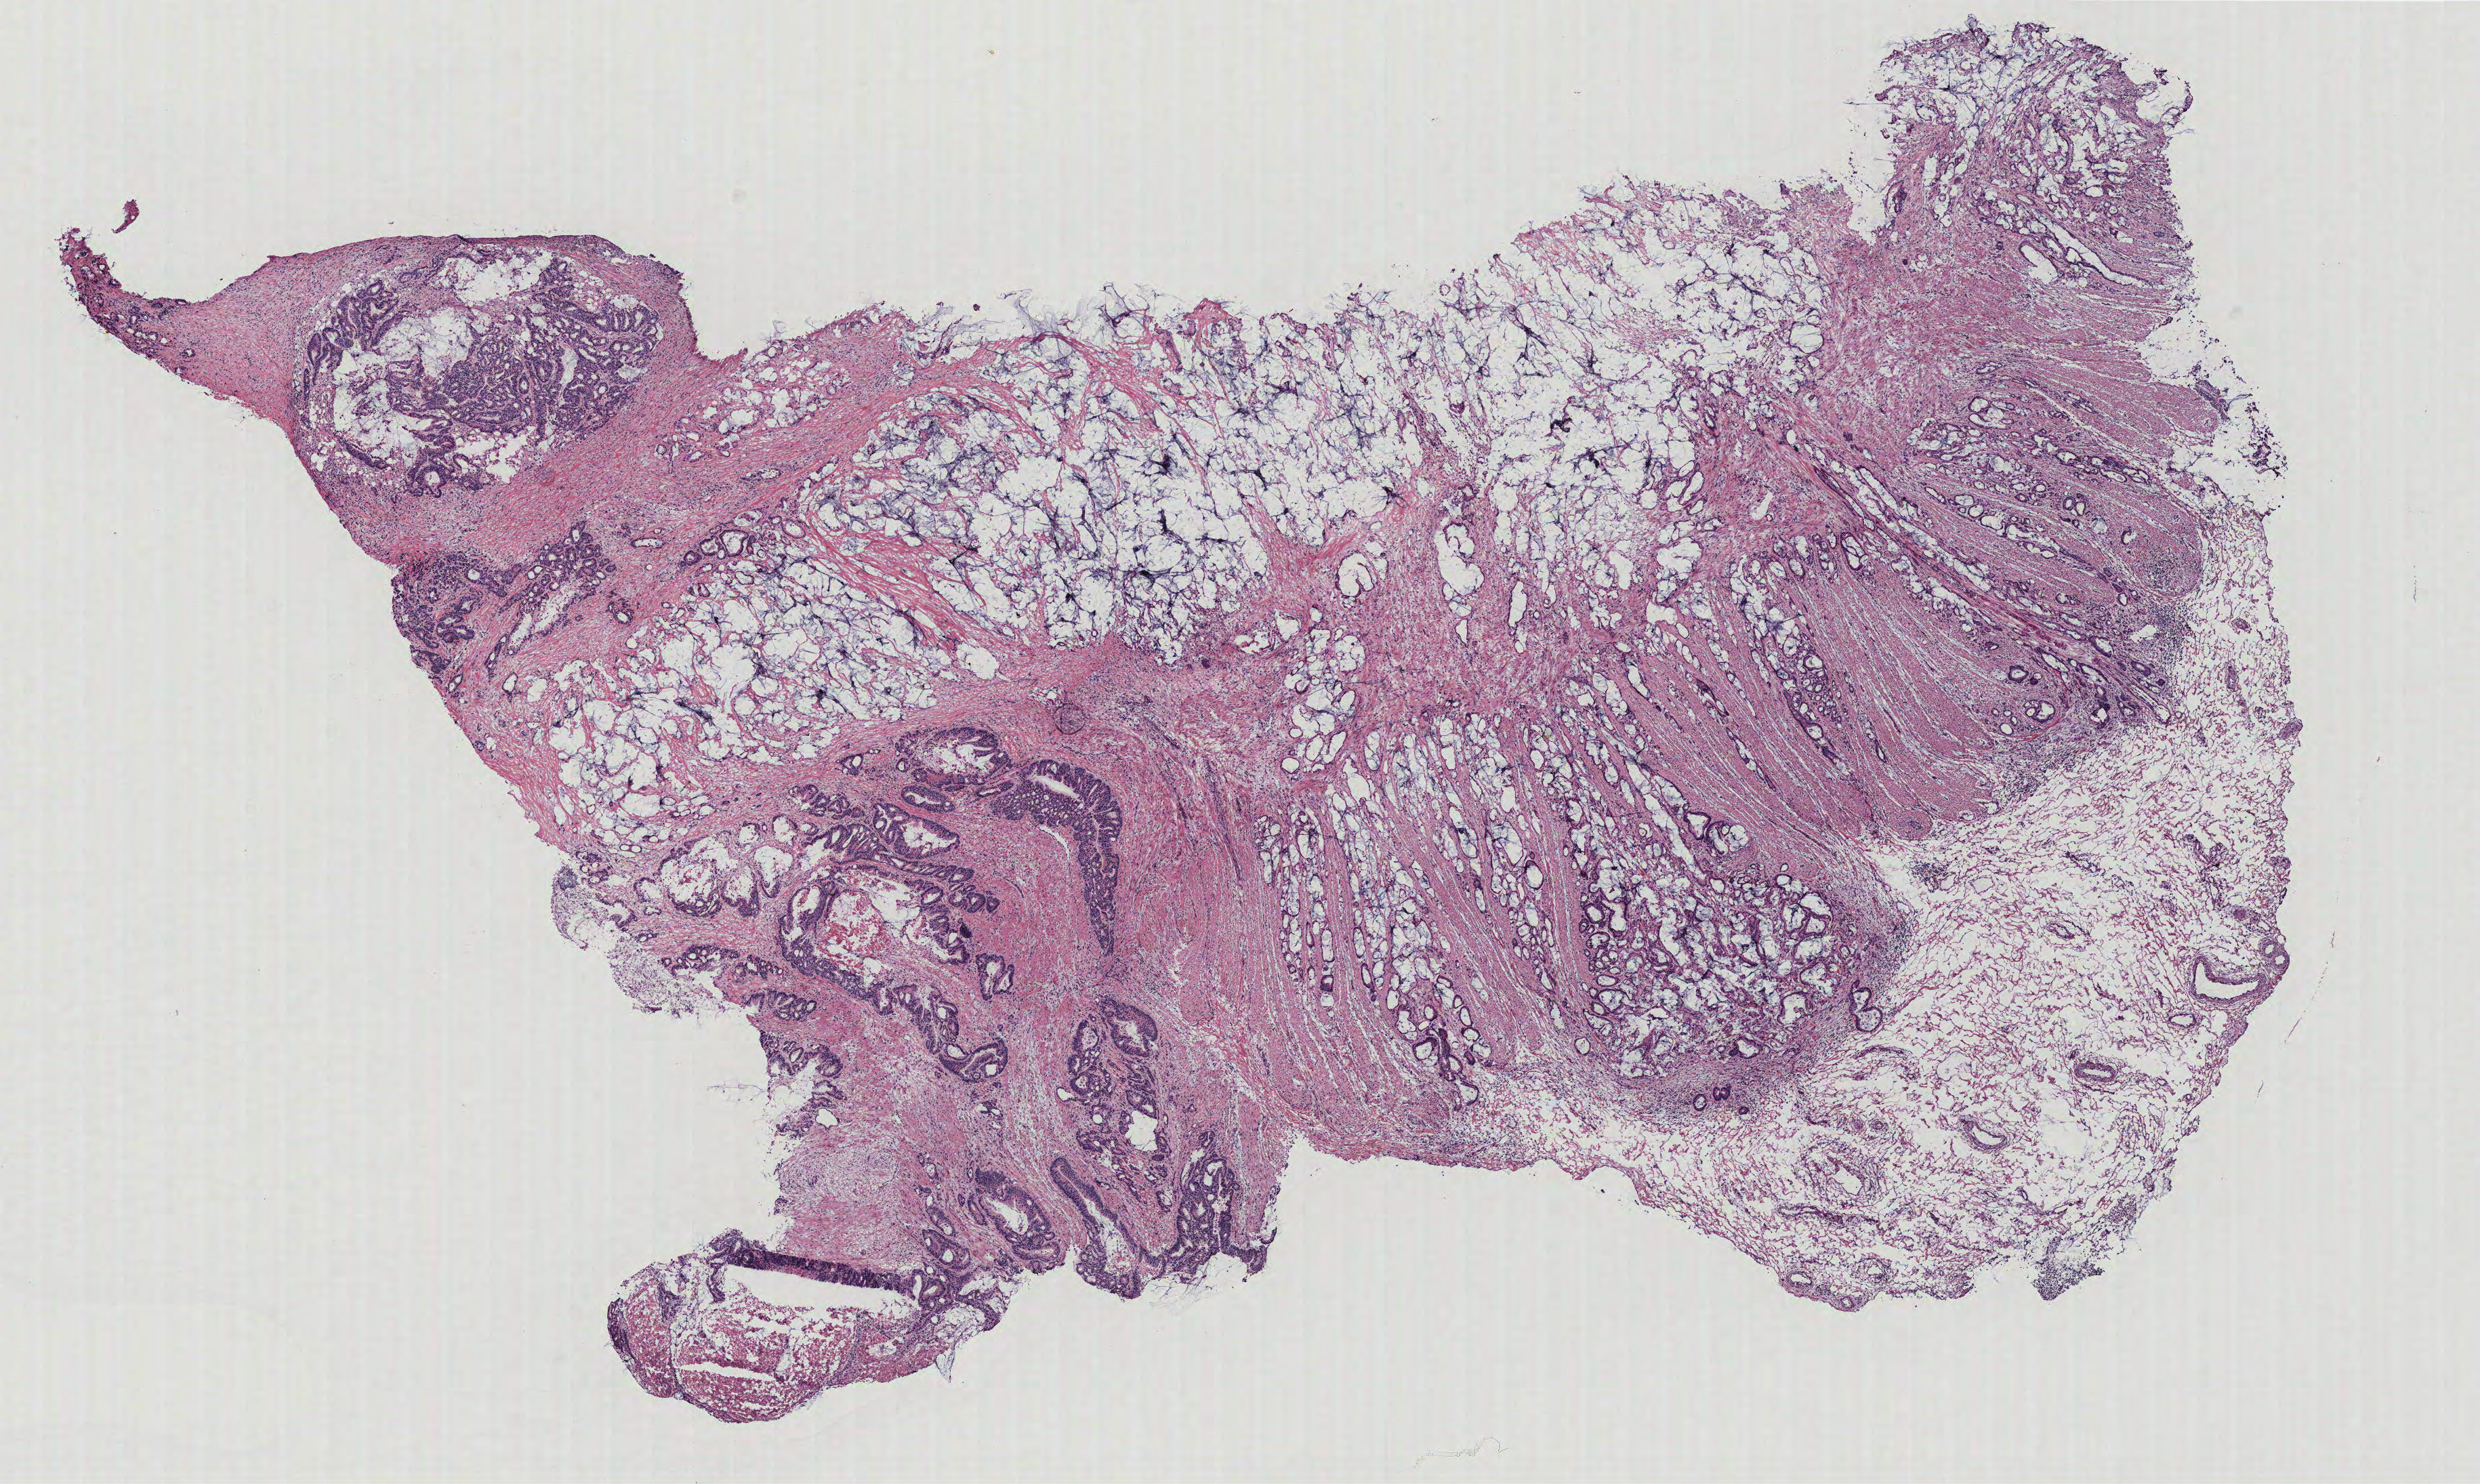
Digitized H&E-stained tissue section (whole slide) — whole scanned area (about 14.6 x 8.8 mm, slide scanned at 40x) shown as a low-resolution overview. Normal (non-tumour) tissue sample, colon. 75-year-old female patient.
This section: normal (non-tumour) tissue from the same patient. Patient diagnosis: Adenocarcinoma, NOS.